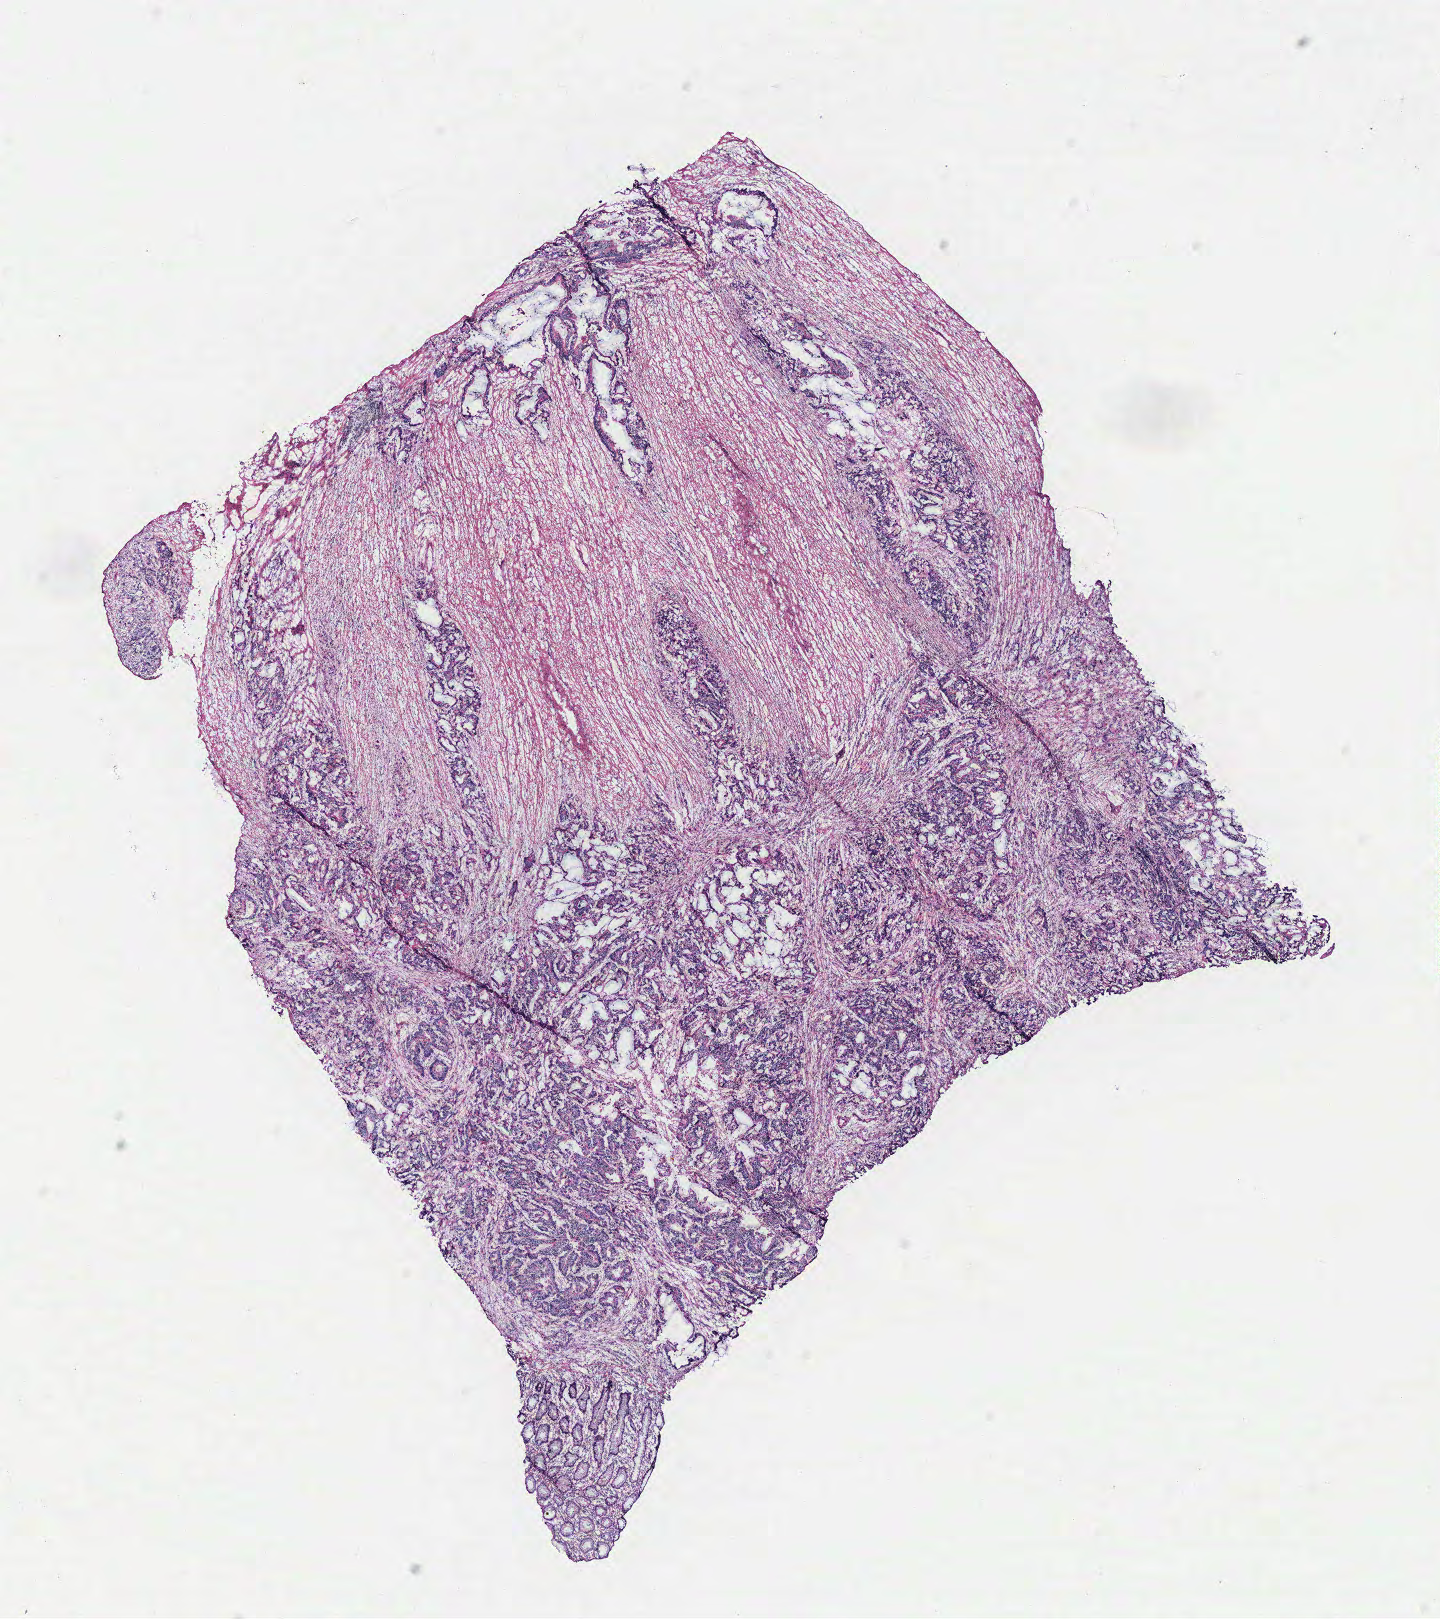
Whole-slide histology image, H&E-stained, shown as a low-resolution overview of the whole scanned area (about 11.5 x 13.0 mm, slide scanned at 40x); tumour tissue sample, colon. Male, 70 y/o.
Patient diagnosis (cohort enrolment): colon cancer (colon).